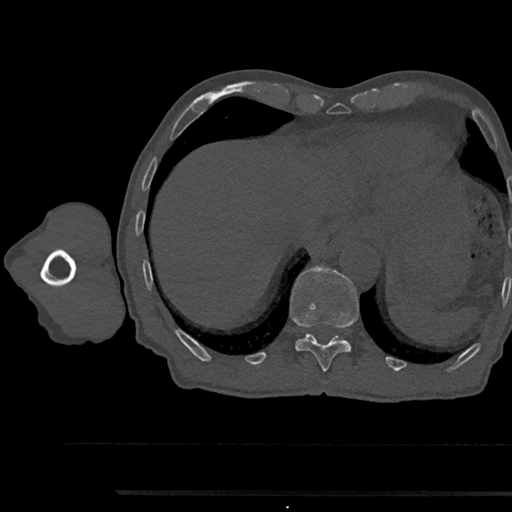
CT including the spine, one axial slice. Slice 777 of 797 in the series (ordered by position). Bone window (W 1800 / L 400 HU). 0.5 mm slice thickness. 512 × 512 image matrix, field of view 367 × 367 mm. Patient: male, 79 years. From the clinical record (not read from this slice): primary cancer: prostate.
Annotated regions visible in this slice (semi-automatic segmentation, software-assisted and operator-edited):
- T11 vertebra: bounding box <290,266,359,373> (left, top, right, bottom; pixels)